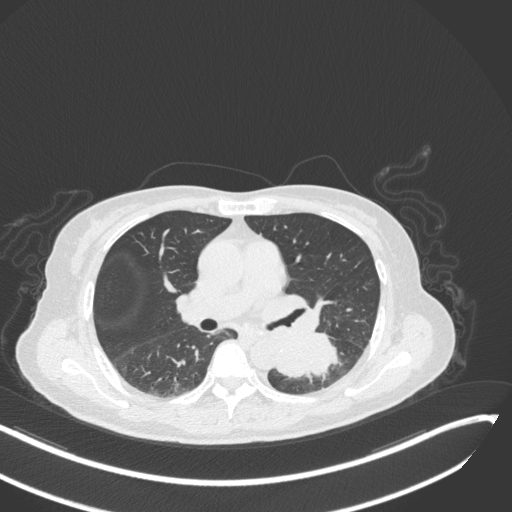
Chest CT, one axial slice. Slice 157 of 342 in the series (ordered by position). Reconstruction kernel B31f. 120 kVp. Lung window (W 1500 / L -600 HU). 1 mm slice thickness. 512 × 512 image matrix. Patient: female, 64 years. From the clinical record (not read from this slice): clinical TNM (as recorded): T3 N1 M1; histopathological grade: G3.
Structures marked on this image (bounding box drawn by a radiologist):
- lung tumour (recorded histology: small cell carcinoma): bounding box (x1, y1, x2, y2) in pixels: (272, 328, 346, 381)